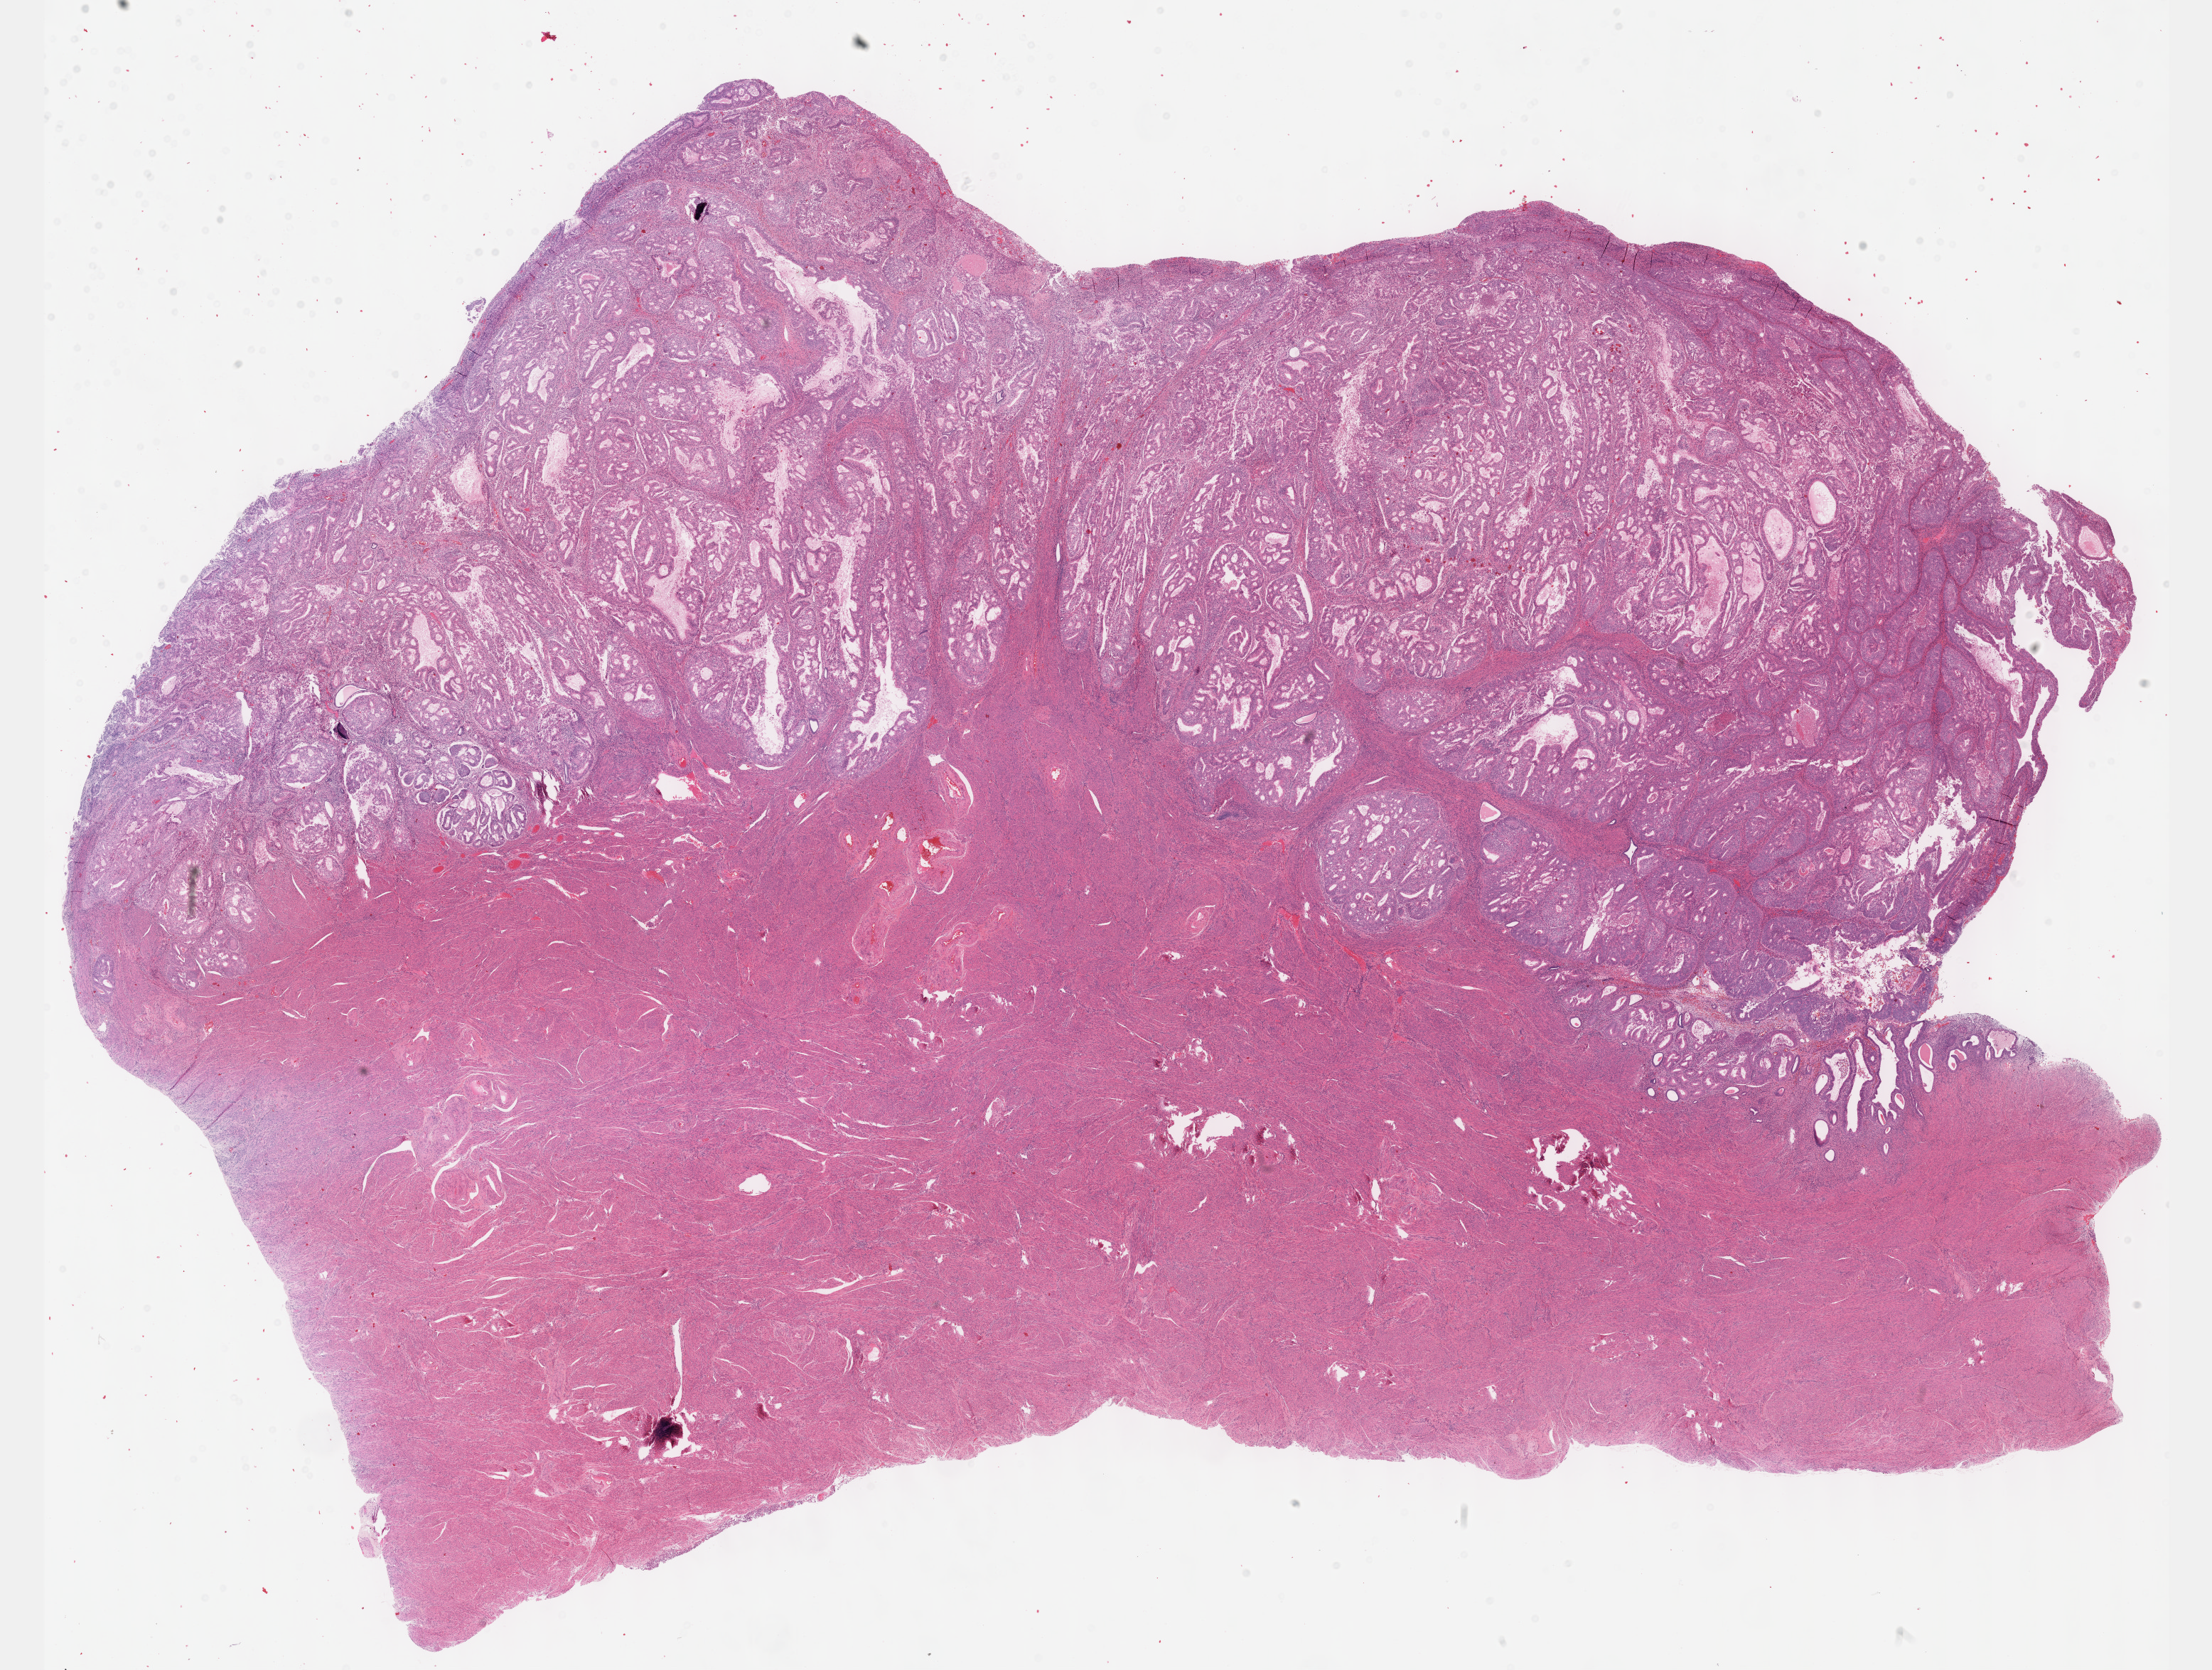
Hematoxylin and eosin (H&E) stained whole-slide image, shown as a low-resolution overview of the whole scanned area (about 25.1 x 19.0 mm, from a 40x scan); FFPE section; uterus, primary tumour sample. Female, age 70 years at initial diagnosis. Histologic grade: G2 (moderately differentiated).
Diagnosis: Endometrioid adenocarcinoma, NOS (endometrium). FIGO stage: I.